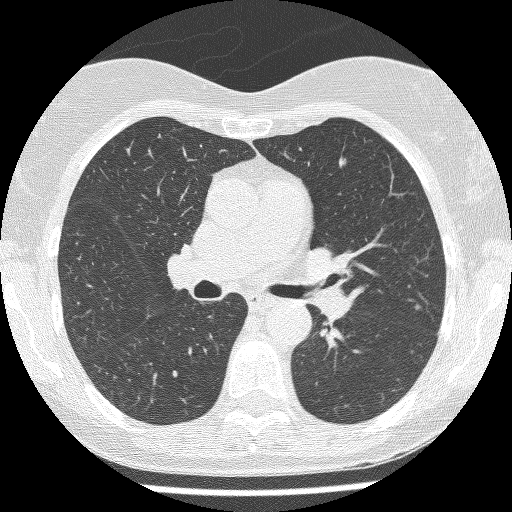
Chest CT (low-dose screening protocol), one axial image; first (baseline) screen; lung window (W 1500 / L -600 HU); 1.25 mm slice thickness; slice 149 of 237 in the series; 512 × 512 image matrix. Female participant, aged 60 years at enrolment. Current smoker at enrolment.
2 expert-annotated lung lesions on this slice (largest first), bounding box (x1, y1, x2, y2) in pixels: (326, 148, 362, 174); (407, 292, 435, 321). Reader record for this screening exam (exam-level; its link to the box is not recorded): non-calcified nodule or mass ≥4 mm, lingula, 5 × 4 mm, smooth margins, soft tissue attenuation. Official screen result: positive, change unspecified: nodule(s) >= 4 mm or enlarging nodule(s), mass(es), or other non-specific abnormalities suspicious for lung cancer. Later outcome: lung cancer diagnosed 790 days after this screen — adenocarcinoma, NOS, left upper lobe, moderately differentiated (G2), stage IA (AJCC 6th edition), 6 mm at pathology.